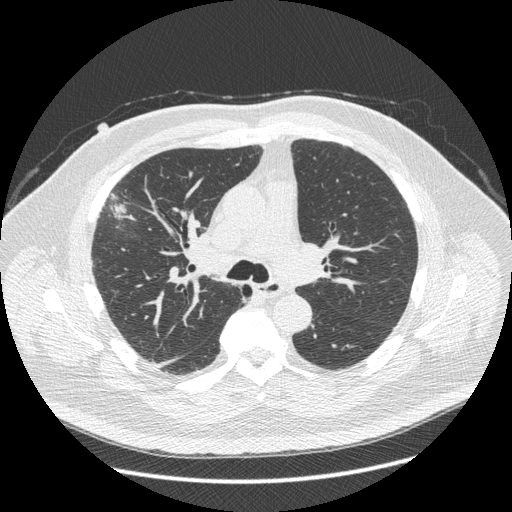
Axial slice from a low-dose chest CT screening exam, third annual screen, lung window (W 1500 / L -600 HU), 1.25 mm slice thickness, slice 157 of 426 in the series, 512 × 512 image matrix. Male, age 66 years at enrolment. Current smoker at enrolment.
Expert reader's lesion annotation, bounding box <85,176,145,264> (left, top, right, bottom; pixels). Reader record for this screening exam (exam-level; its link to the box is not recorded): non-calcified nodule or mass ≥4 mm, right upper lobe, 48 × 25 mm, spiculated (stellate) margins, soft tissue attenuation, pre-existing on the prior screen: no. Lung cancer was diagnosed 35 days after this screen: non-small cell carcinoma, right upper lobe, stage IV (AJCC 6th edition), 50 mm at pathology.